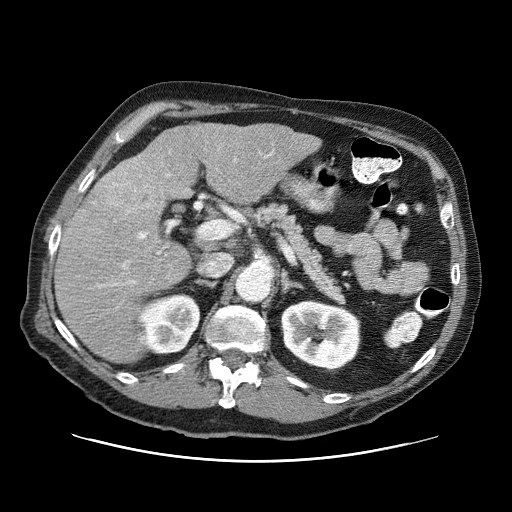
Contrast-enhanced abdominal CT (liver protocol), one axial slice. Position 38 of 87 along the scan axis. Reconstruction kernel STANDARD. 120 kVp. One of 3 acquisitions stored at this slice position. Soft-tissue window (W 400 / L 40 HU). 512 × 512 image matrix, field of view 400 × 400 mm. Case-level facts recorded for this patient, not image findings: diagnosis: hepatocellular carcinoma (patient treated with transarterial chemoembolisation; whether this scan precedes or follows treatment is not stated here); TNM stage (as recorded): Stage-IIIA; Child-Pugh class: A; tumour differentiation: well differentiated; tumour size: 6 cm.
Outlined on this slice (semi-automatically segmented with operator editing):
- liver parenchyma outside the tumour (the mass and vessels are separate outlines, so this box may not span the whole liver): bounding box <54,124,320,362> (left, top, right, bottom; pixels)
- mass: <87,160,165,229>
- liver vessels: <99,153,272,288>